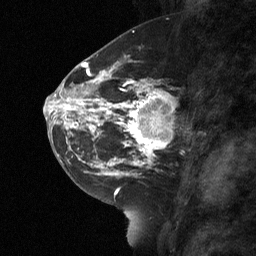
Breast MRI (dynamic contrast-enhanced), one sagittal slice; slice 31 of 64 in the series (ordered by position); dynamic contrast-enhanced study with each time point stored as its own series, time point 2 of 3 at this slice position (early post-contrast, ordered by acquisition time); 1.5 T; TE 4.8 ms, TR 27 ms; 2 mm slice thickness; 256 × 256 image matrix, field of view 180 × 180 mm. Female patient, age 42 years. From the clinical record (not read from this slice): setting: breast cancer imaged before/during neoadjuvant chemotherapy; receptor status: triple-negative.
Annotated regions visible in this slice (semi-automatic segmentation, software-assisted and operator-edited):
- analysis volume of interest (the breast-tissue region the enhancement analysis was run in; not a lesion): box from (x=115, y=85) to (x=190, y=160) px
- tumour enhancement mask (voxels above the 90 % enhancement threshold inside the analysis volume of interest): (x=115, y=85)–(x=171, y=160)